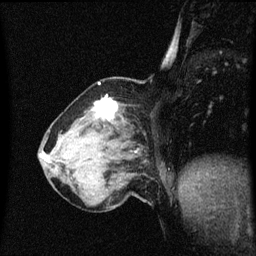
Breast MRI (dynamic contrast-enhanced), one sagittal slice. Dynamic contrast-enhanced series, image 2 of 3 at this slice position (ordered by acquisition). 1.5 T. TE 4.2 ms, TR 8.4 ms. 2 mm slice thickness. 256 × 256 image matrix. Patient: female, 64 years. From the clinical record (not read from this slice): setting: breast cancer imaged before/during neoadjuvant chemotherapy; receptor status: HR-positive, HER2-negative.
Structures marked on this image (semi-automatic segmentation, software-assisted and operator-edited):
- analysis volume of interest (the breast-tissue region the enhancement analysis was run in; not a lesion): box from (x=58, y=96) to (x=143, y=167) px
- tumour enhancement mask (voxels above the 70 % enhancement threshold inside the analysis volume of interest): (x=96, y=98)–(x=117, y=121)